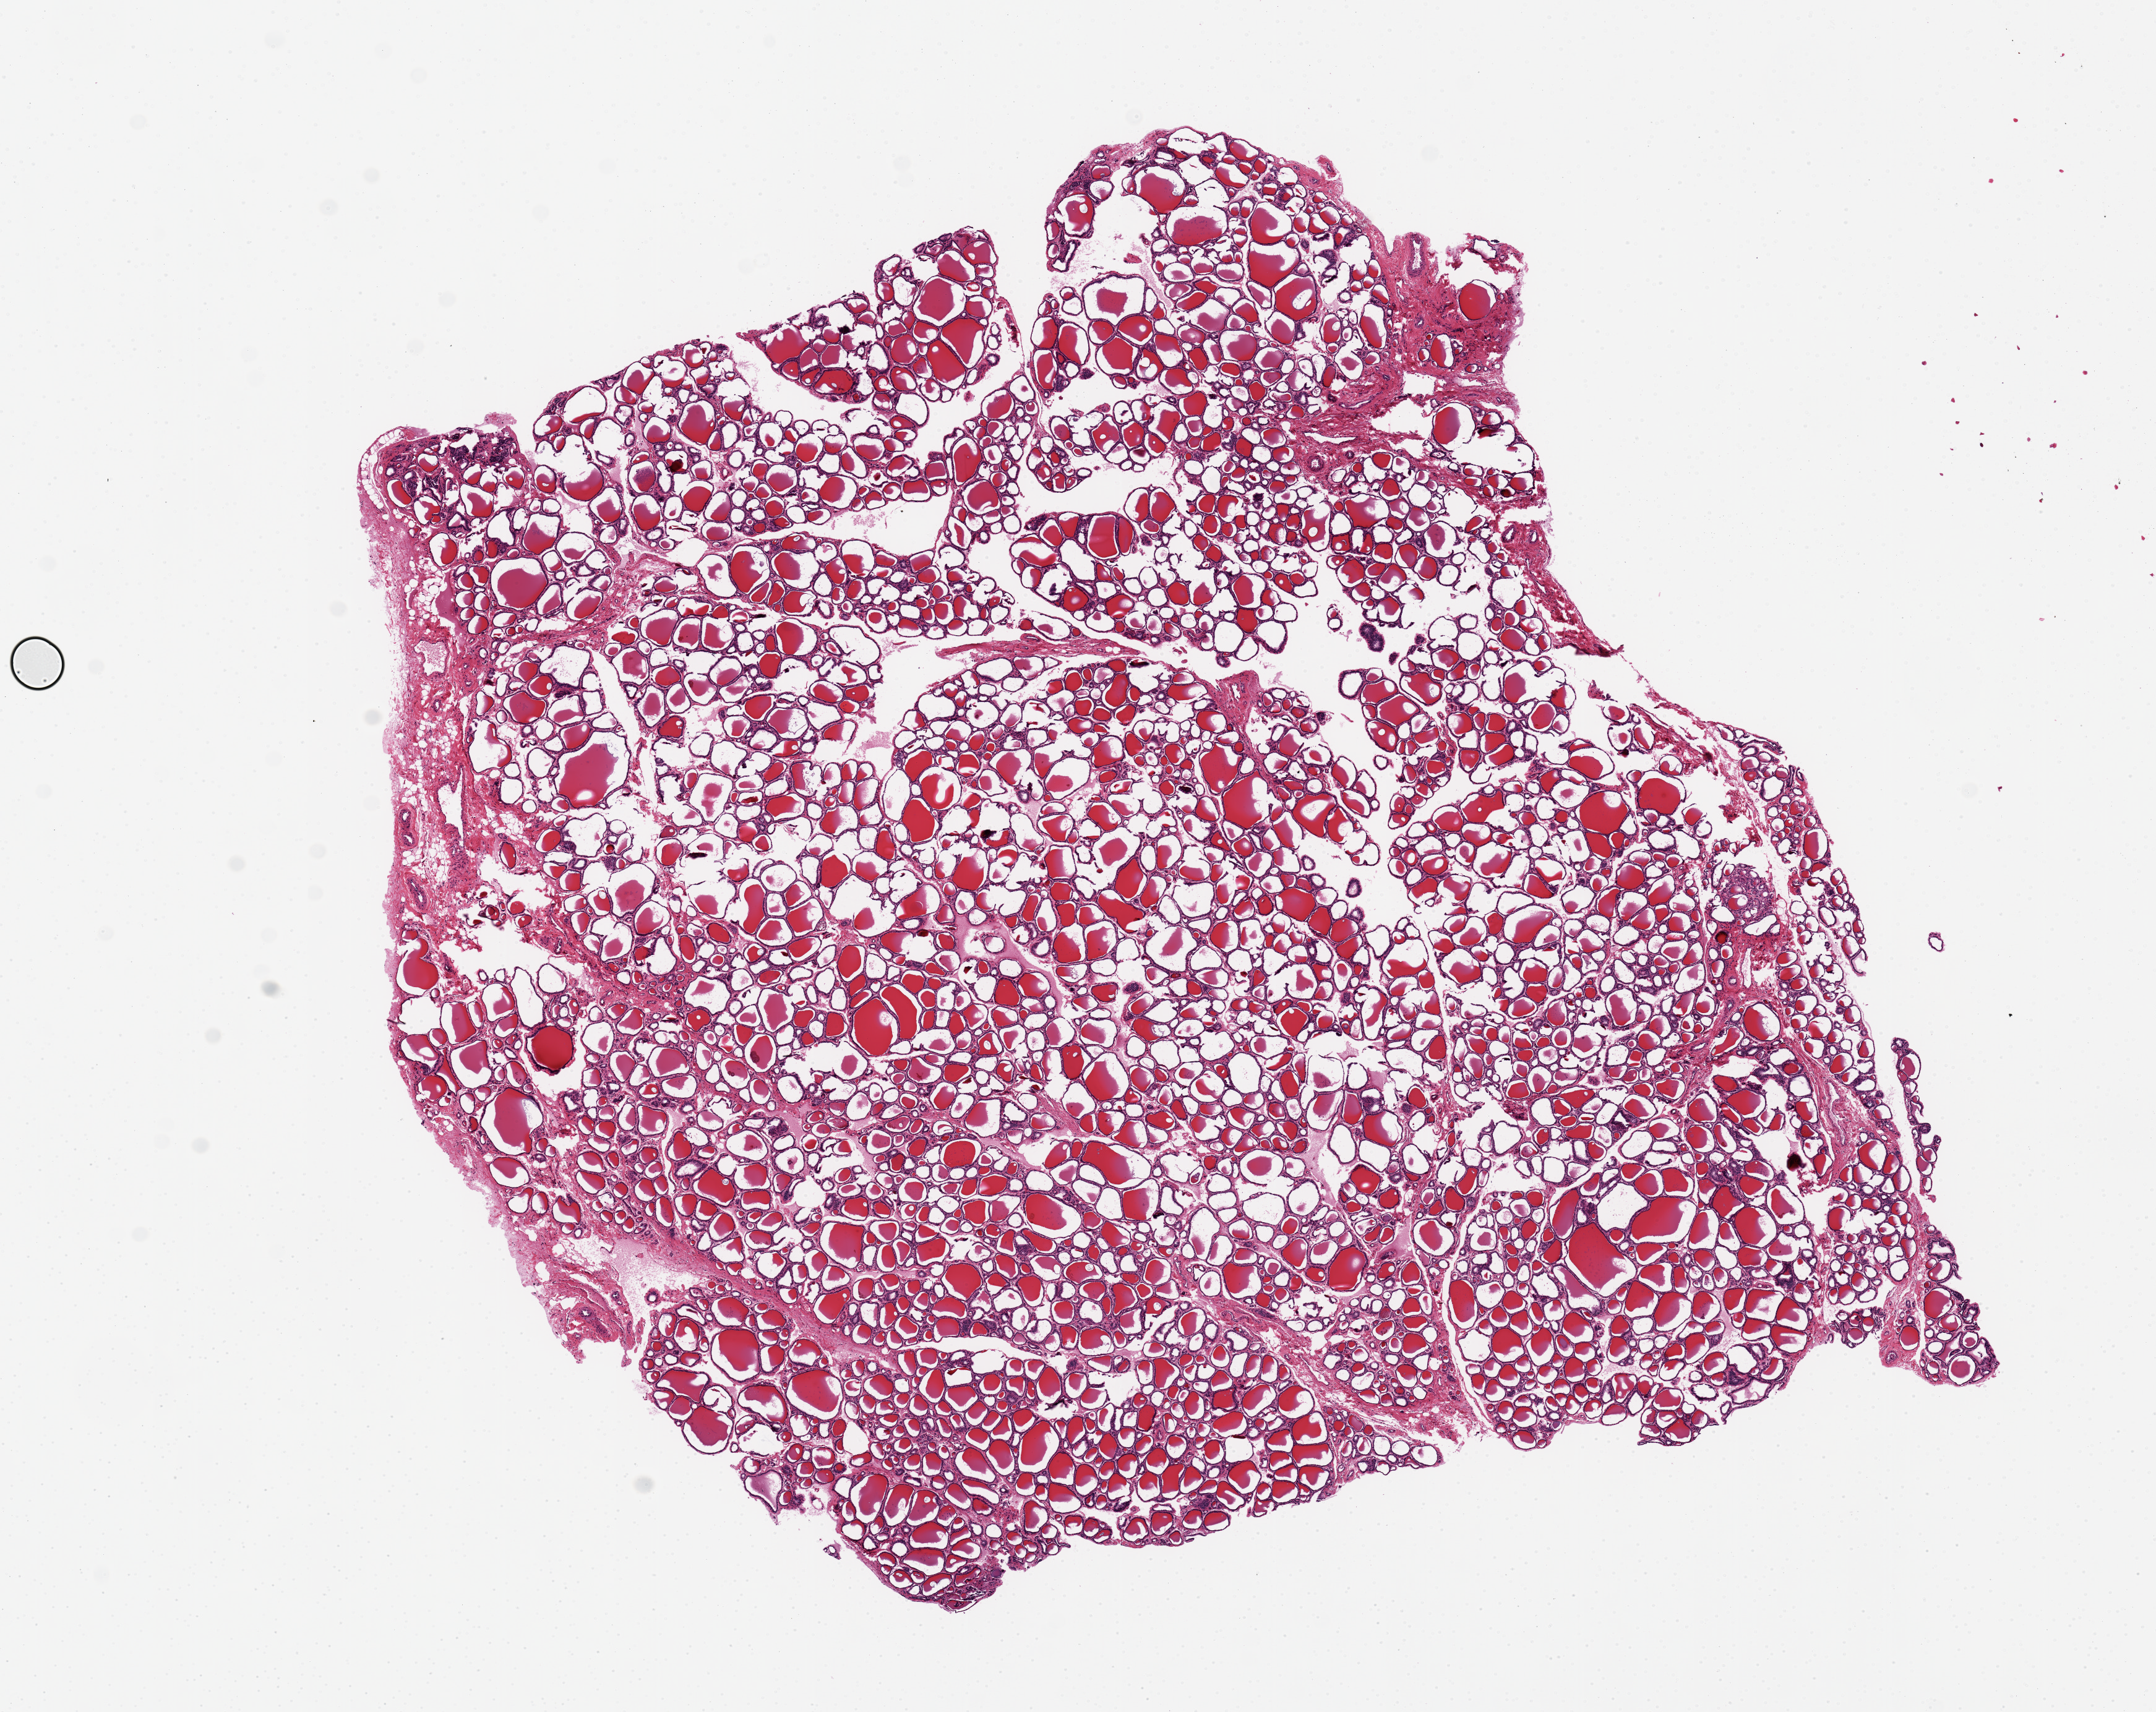
Hematoxylin and eosin (H&E) whole-slide image — shown as a low-resolution overview of the whole scanned area (about 13.8 x 10.9 mm), PAXgene-fixed paraffin-embedded (PFPE) section, sampled site (target tissue): thyroid, donor tissue sample. Donor sex: male.
Review note (as recorded): Reasonably well preserved for endocrine organ.